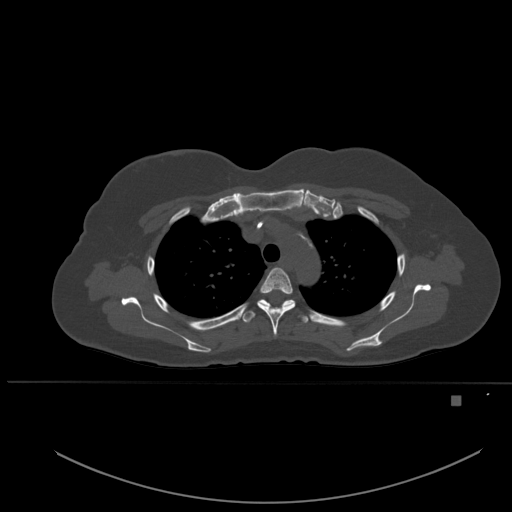
CT including the spine, one axial slice; slice 389 of 651 in the series (ordered by position); bone window (W 1800 / L 400 HU); 1.5 mm slice thickness; 512 × 512 image matrix, field of view 443 × 443 mm. Female patient, age 49 years. Case-level facts recorded for this patient, not image findings: primary cancer: breast.
Outlined on this slice (semi-automatic segmentation, software-assisted and operator-edited):
- T3 vertebra: bounding box <257,268,295,337> (left, top, right, bottom; pixels)
- T4 vertebra: <239,299,309,323>